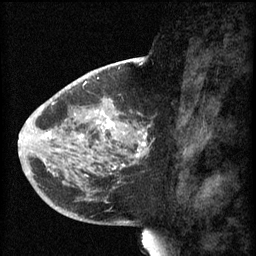
Breast MRI (dynamic contrast-enhanced), one sagittal slice. Position 27 of 60 along the scan axis. 3 images stored at this slice position (order not interpretable as contrast timing). 1.5 T. TE 4.2 ms, TR 8.1 ms. 256 × 256 image matrix. Female patient, age 44 years.
Annotated regions visible in this slice (semi-automatically segmented with operator editing):
- analysis volume of interest (the breast-tissue region the enhancement analysis was run in; not a lesion): bounding box (x1, y1, x2, y2) in pixels: (59, 110, 151, 169)
- tumour enhancement mask (voxels above the 70 % enhancement threshold inside the analysis volume of interest): (74, 112, 150, 169)